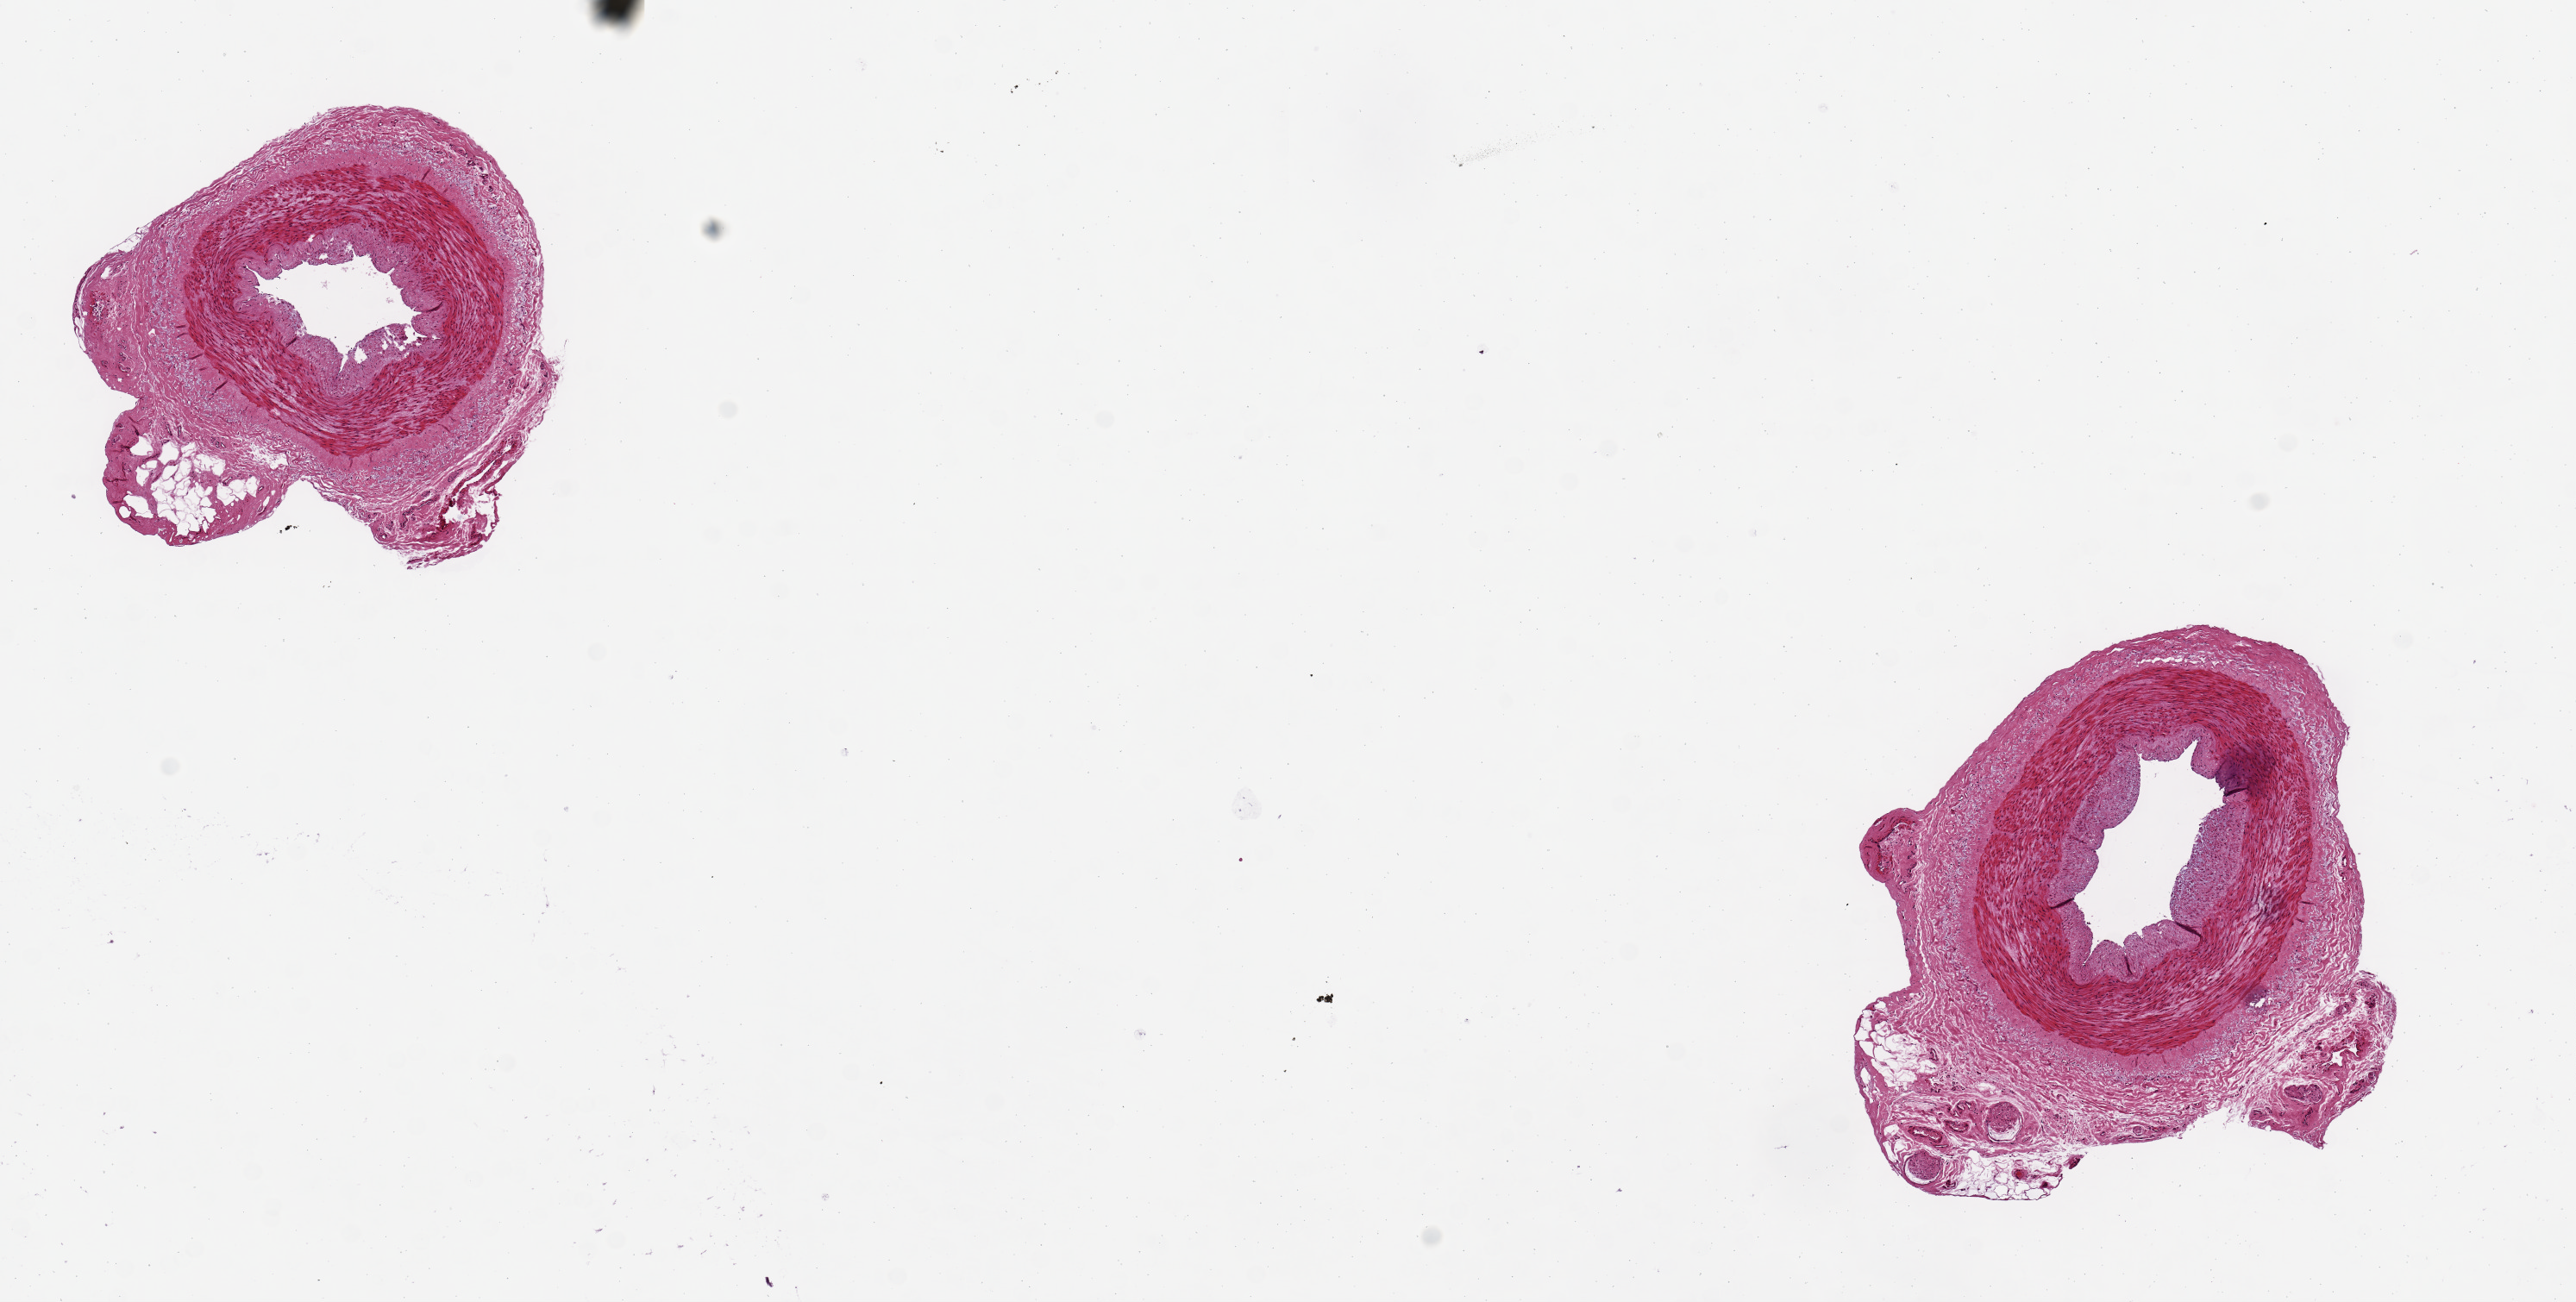
Whole-slide image, H&E stain, shown as a low-resolution overview of the whole scanned area (about 11.8 x 6.0 mm, slide scanned at 20x), PAXgene-fixed, paraffin-embedded tissue, sampled site (target tissue): tibial artery, donor tissue sample. Female donor.
Review note (as recorded): 2 pieces 2 mm artery.